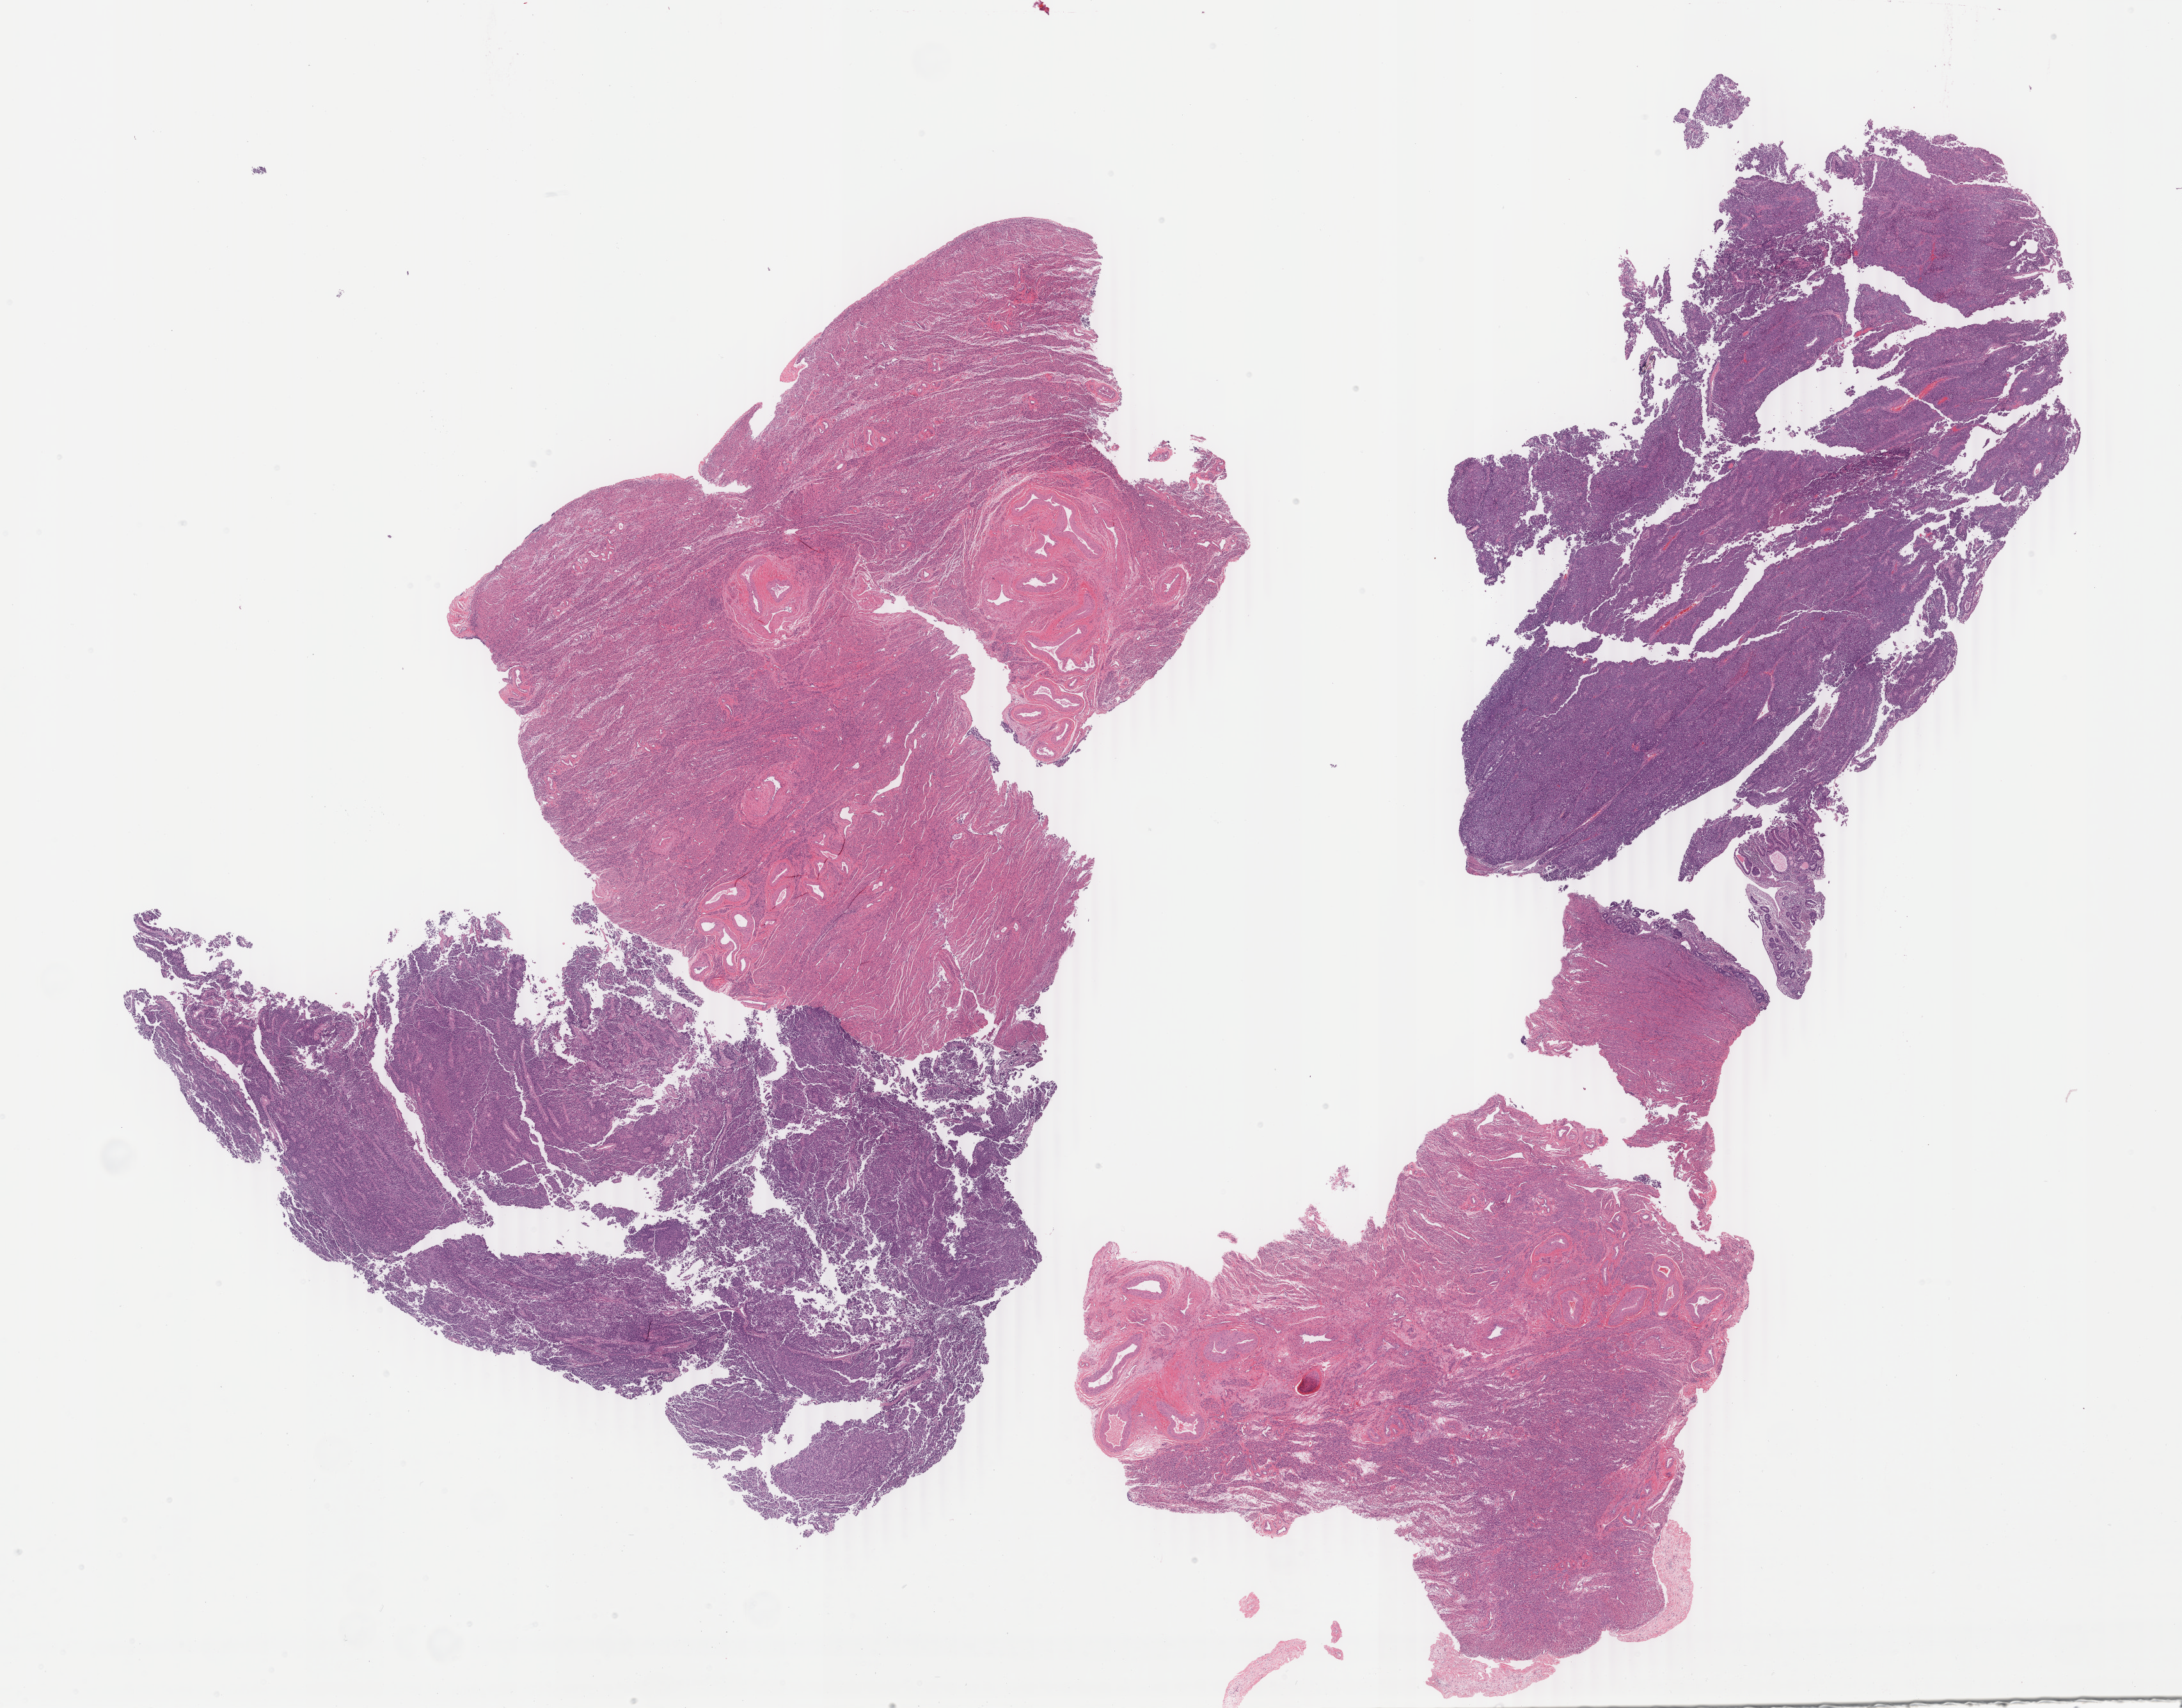
Digitized H&E-stained tissue section (whole slide), shown as a low-resolution overview of the whole scanned area (about 27.1 x 21.2 mm), formalin-fixed paraffin-embedded (FFPE) diagnostic section, sample: primary tumour, uterus. Female, age 58 years at initial diagnosis.
Diagnosis: Endometrioid adenocarcinoma, NOS (endometrium).